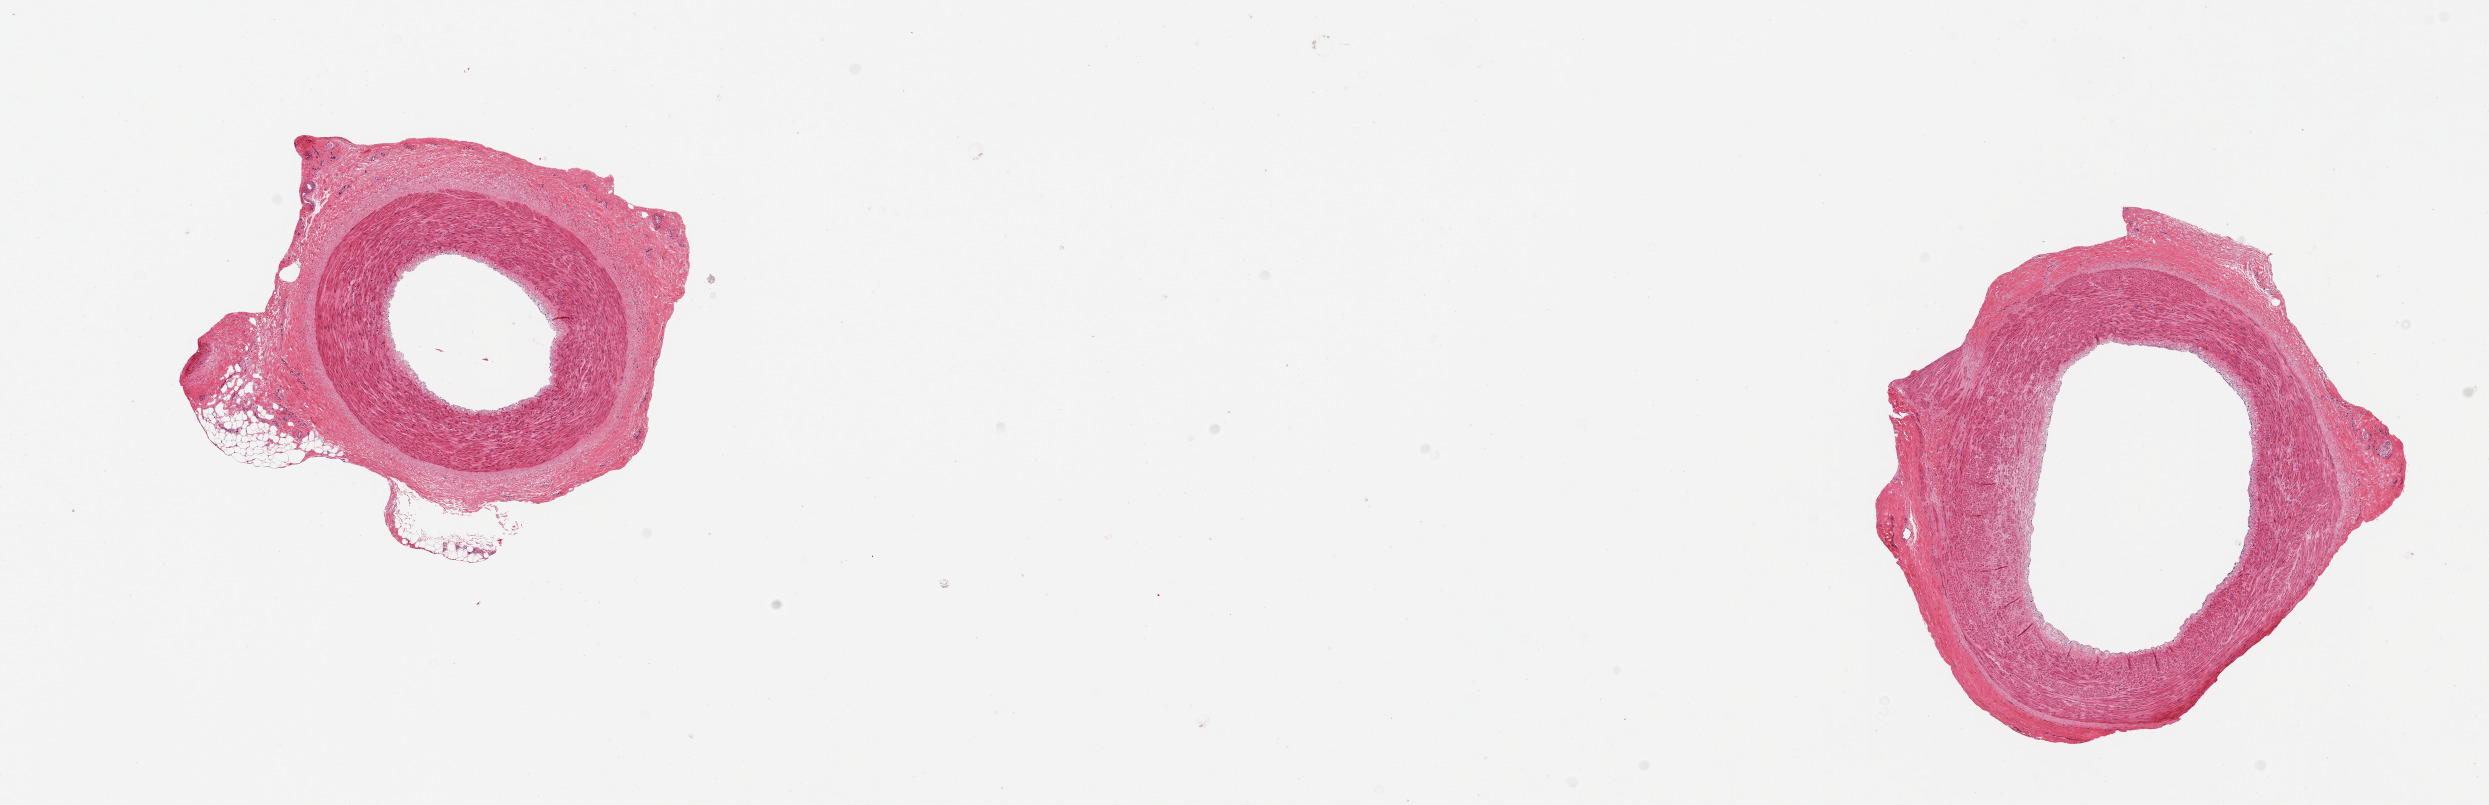
Whole-slide image, hematoxylin and eosin (H&E) stain, brightfield, whole scanned area (about 19.7 x 6.4 mm) shown as a low-resolution overview; PAXgene-fixed paraffin-embedded (PFPE) section; section of tibial artery (target tissue); donor tissue sample. Donor: female.
- review note (as recorded): 2 pieces; no lesions